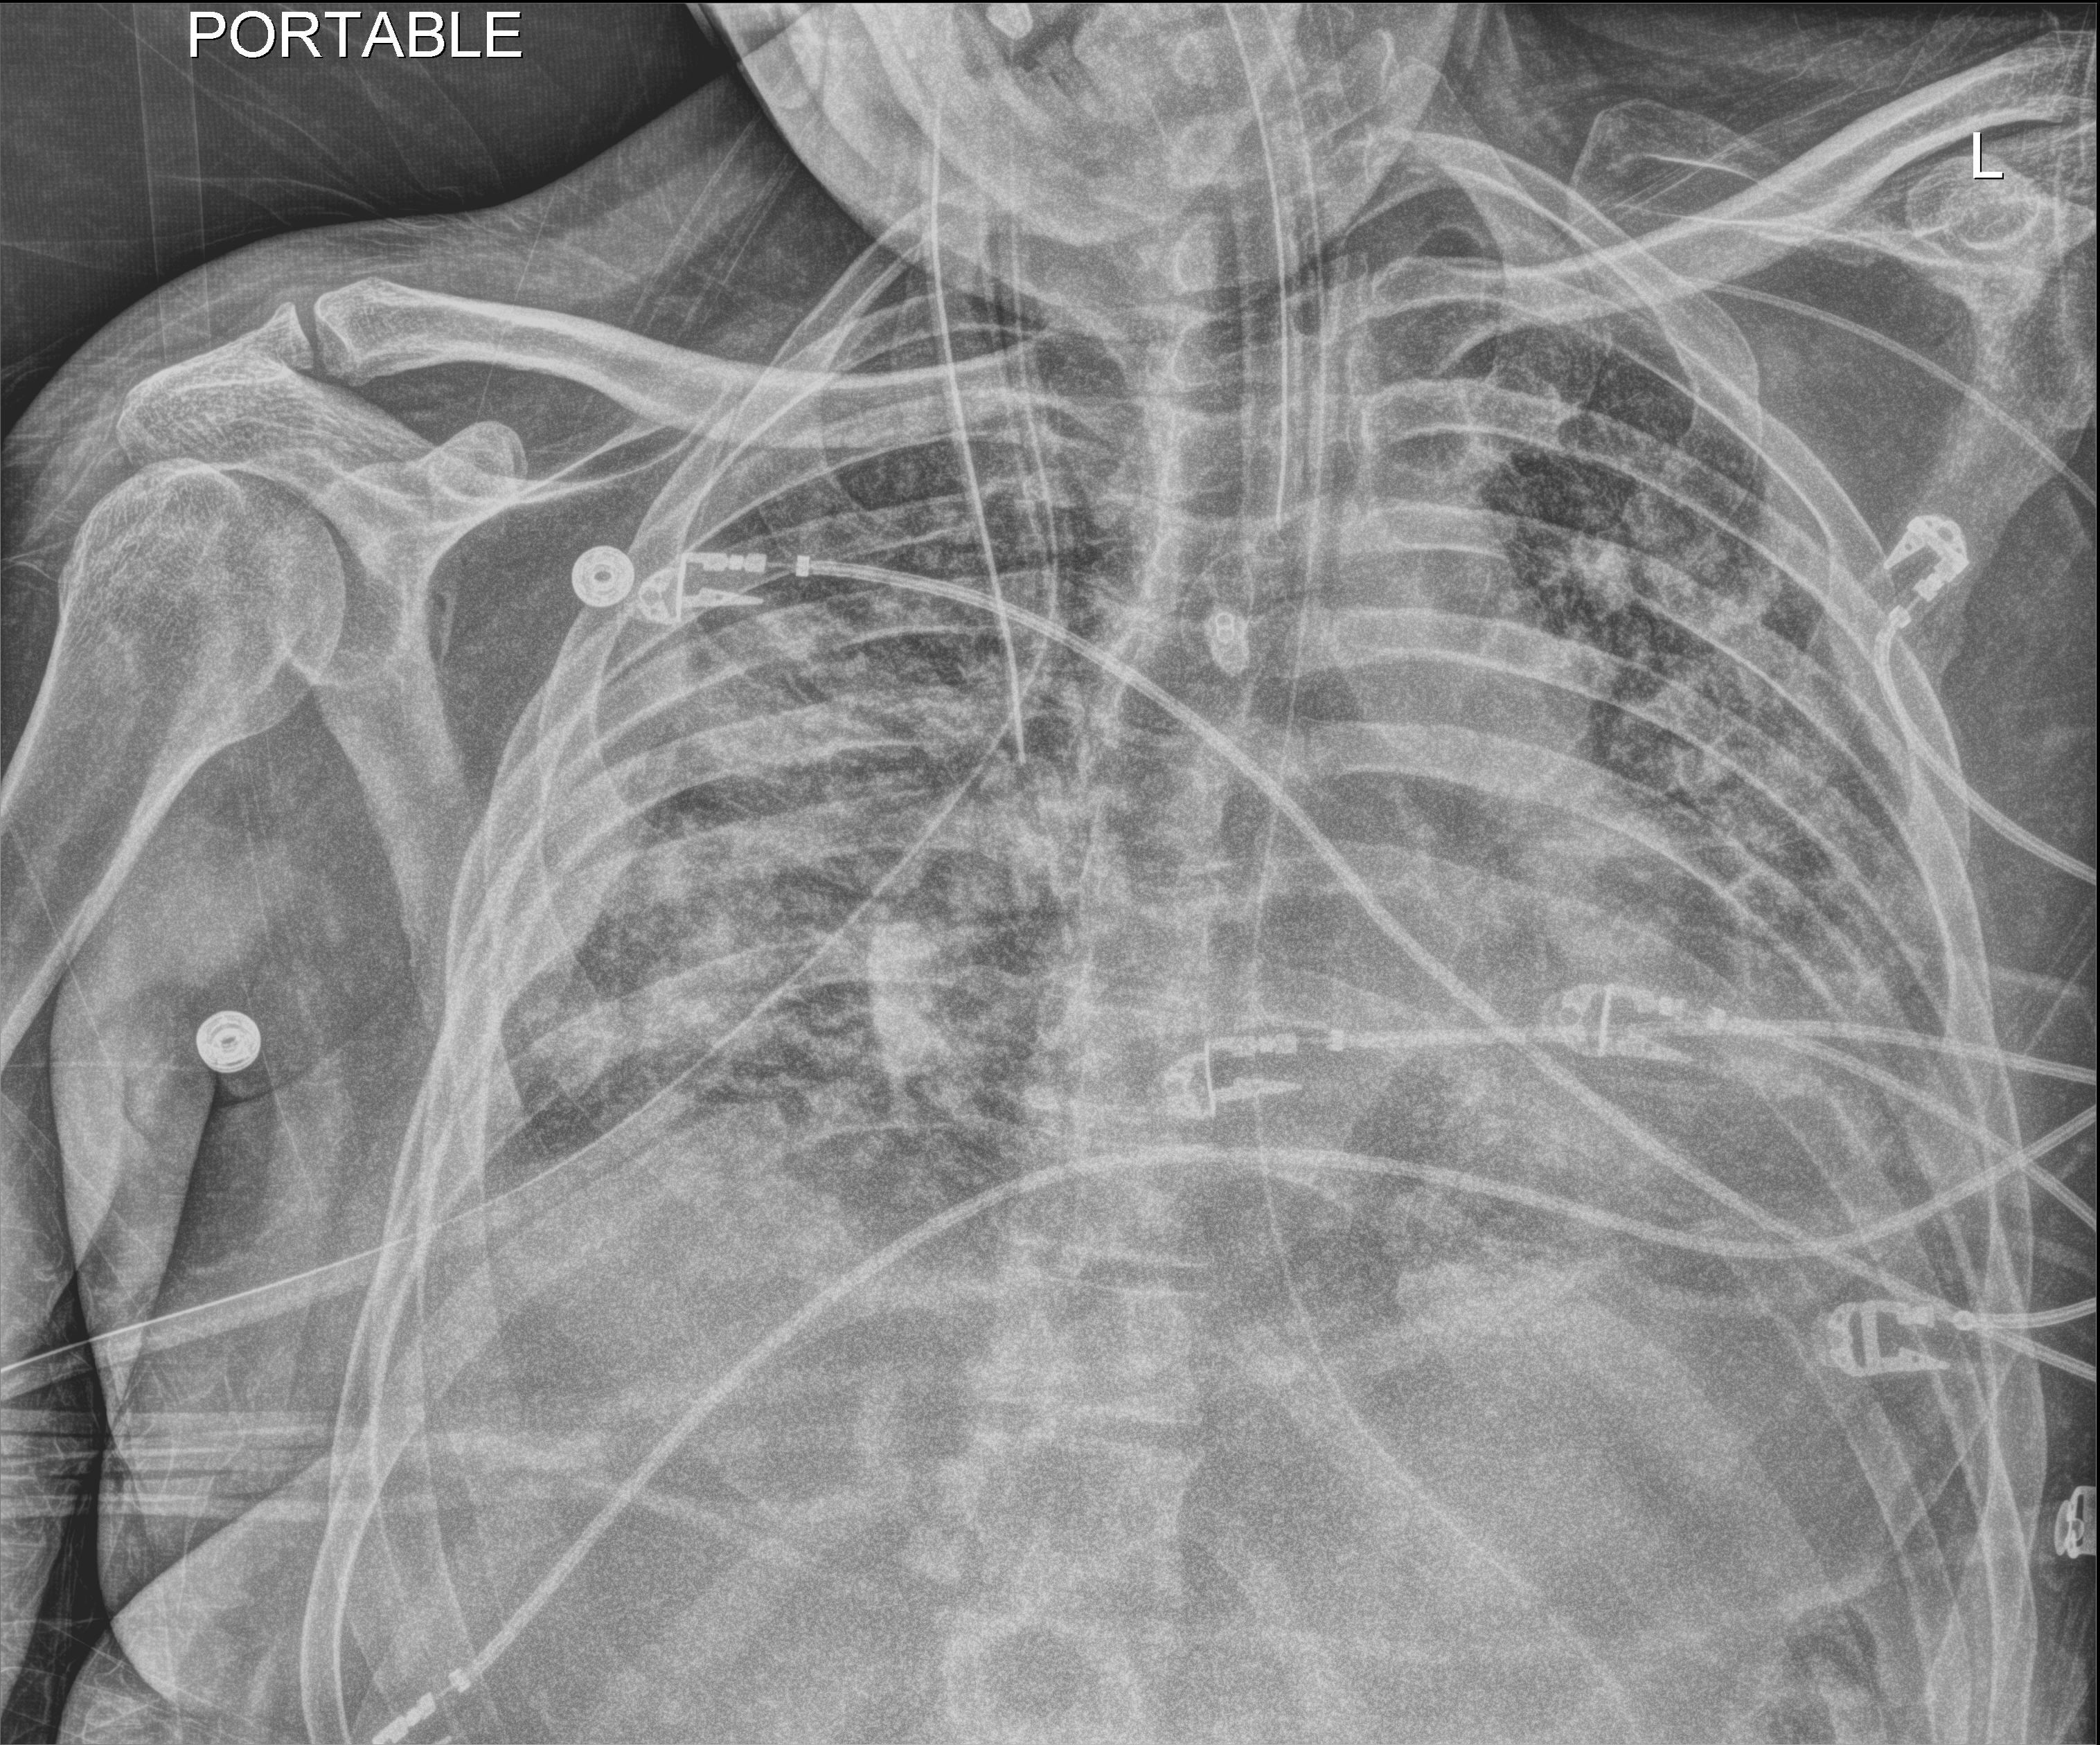
Chest X-ray (portable), anteroposterior (AP) projection. Male patient hospitalised with COVID-19, age 18–59 years.
Hospital-stay facts (about this admission, not read from this image; timing relative to this image not recorded): mechanically ventilated during this hospital stay: yes; admitted to intensive care during this hospital stay: yes.